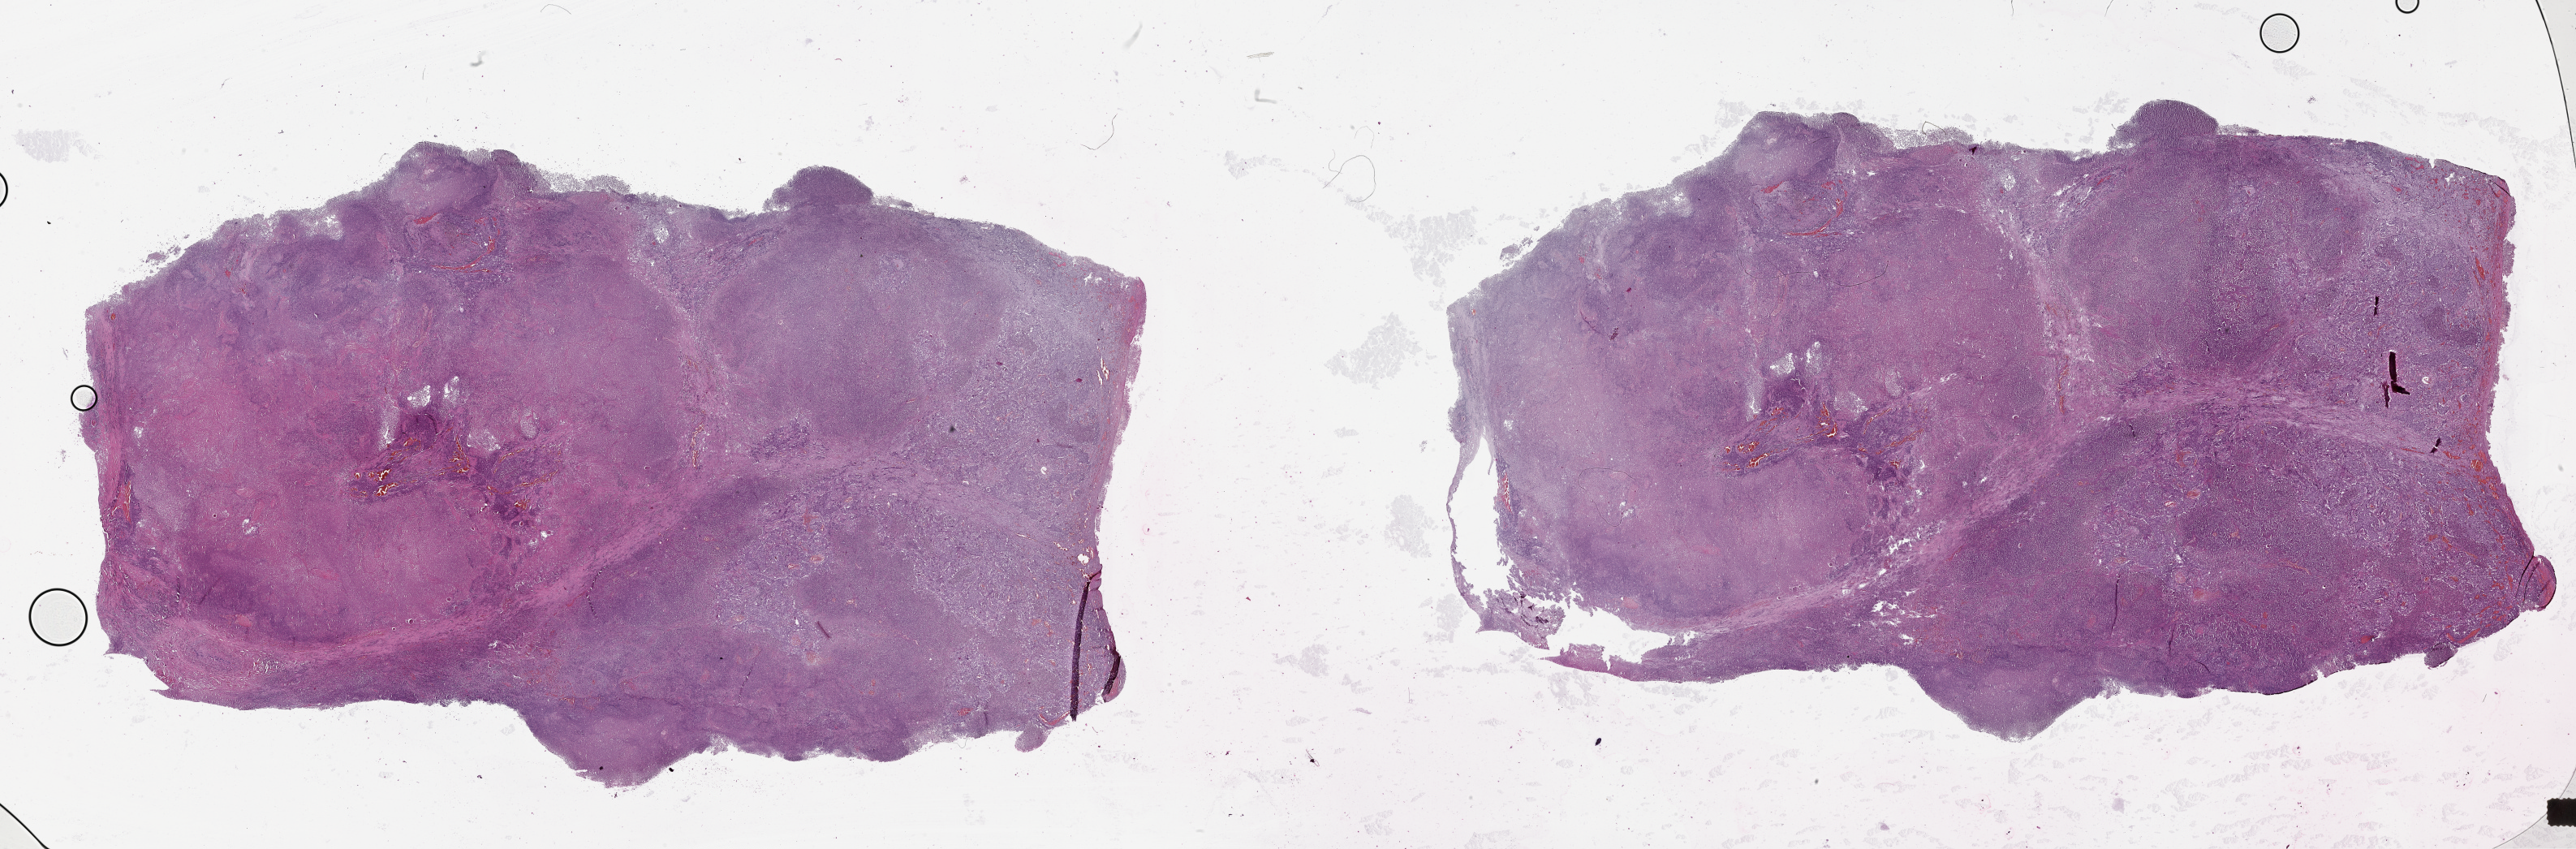
Whole-slide histology image, Hematoxylin and eosin (H&E) stained — whole scanned area (about 51.1 x 16.8 mm) shown as a low-resolution overview. Lung, tumour tissue. Patient: male, age 67 years.
• patient diagnosis (cohort enrolment): squamous cell carcinoma (lung)